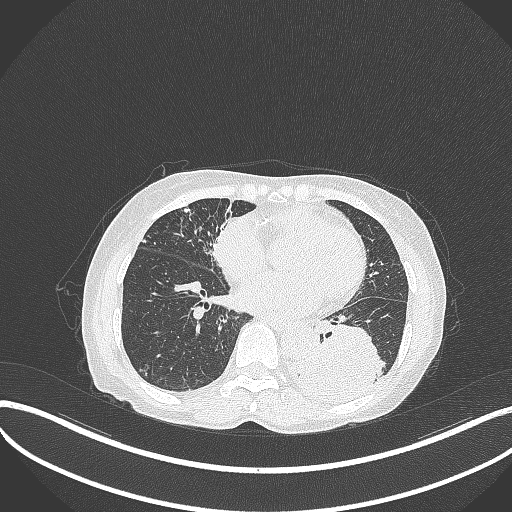
Chest CT, one axial slice. Position 121 of 370 along the scan axis. Reconstruction kernel B70f. 120 kVp. Lung window (W 1500 / L -600 HU). 1 mm slice thickness. 512 × 512 image matrix, field of view 400 × 400 mm. Female patient, age 78 years. From the clinical record (not read from this slice): clinical TNM (as recorded): T3 N0 M1.
Annotated regions visible in this slice (bounding box drawn by a radiologist):
- lung tumour (recorded histology: squamous cell carcinoma): bounding box [x1, y1, x2, y2] px = [295, 315, 383, 400]